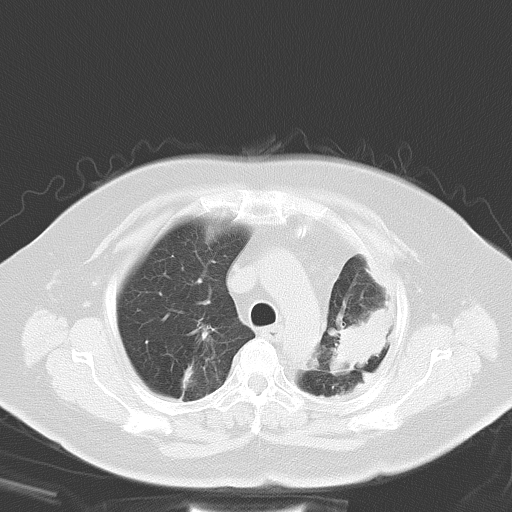
Chest CT, one axial slice. Reconstruction kernel B70f. Lung window (W 1500 / L -600 HU). 8 mm slice thickness. 512 × 512 image matrix, field of view 347 × 347 mm. Patient: female, 69 years. Case-level facts recorded for this patient, not image findings: clinical TNM (as recorded): T3 N0 M0.
Outlined on this slice (rectangle marked by the reading radiologist):
- lung tumour (recorded histology: adenocarcinoma): bounding box (x1, y1, x2, y2) in pixels: (328, 309, 395, 382)